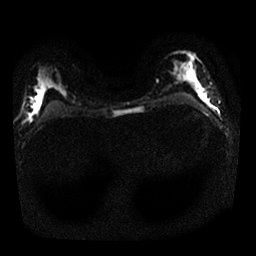
Breast MRI, one axial slice. Position 12 of 25 along the scan axis. Diffusion-weighted series; image 2 of 4 stored at this slice position (different b-values; order by instance number). 1.5 T. 4 mm slice thickness. 256 × 256 image matrix, field of view 320 × 320 mm. Female patient.
Annotated regions visible in this slice (expert manual segmentation):
- tumour on diffusion-weighted imaging: box from (x=202, y=94) to (x=205, y=98) px